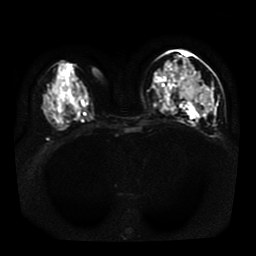
Breast MRI, one axial slice; position 20 of 41 along the scan axis; diffusion-weighted series; image 2 of 4 stored at this slice position (different b-values; order by instance number); 1.5 T; 5 mm slice thickness; 256 × 256 image matrix, field of view 330 × 330 mm. Female patient.
Structures marked on this image (expert manual segmentation):
- tumour on diffusion-weighted imaging: bounding box [x1, y1, x2, y2] px = [179, 79, 212, 114]